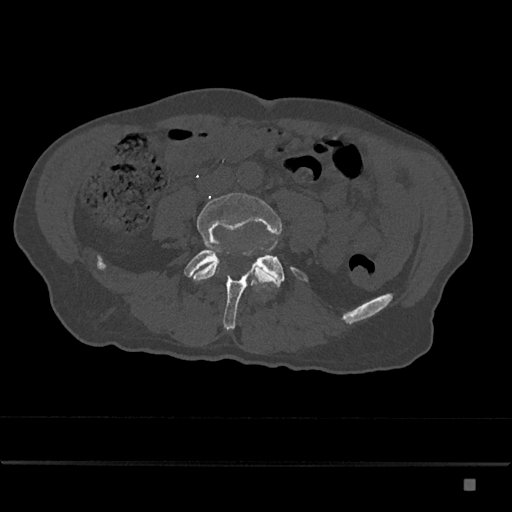
CT including the spine, one axial slice; reconstruction kernel Br40s/3; bone window (W 1800 / L 400 HU); 0.5 mm slice thickness; 512 × 512 image matrix. Patient: male, 72 years. From the clinical record (not read from this slice): primary cancer: prostate.
Annotated regions visible in this slice (semi-automatic segmentation, software-assisted and operator-edited):
- L4 vertebra: bounding box [x1, y1, x2, y2] px = [191, 193, 282, 285]
- L5 vertebra: [184, 241, 308, 330]